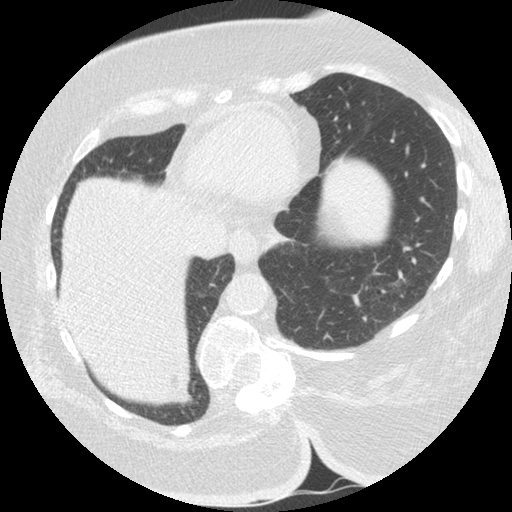
Low-dose screening chest CT, one axial slice. Slice 44 of 151 in the series (ordered by position). Reconstruction kernel STANDARD. Lung window (W 1500 / L -600 HU). 2.5 mm slice thickness. 512 × 512 image matrix, field of view 340 × 340 mm.
Structures marked on this image (expert manual segmentation):
- lesion 1 (tumor, lower lobe of right lung): bounding box (x1, y1, x2, y2) in pixels: (181, 395, 198, 407)